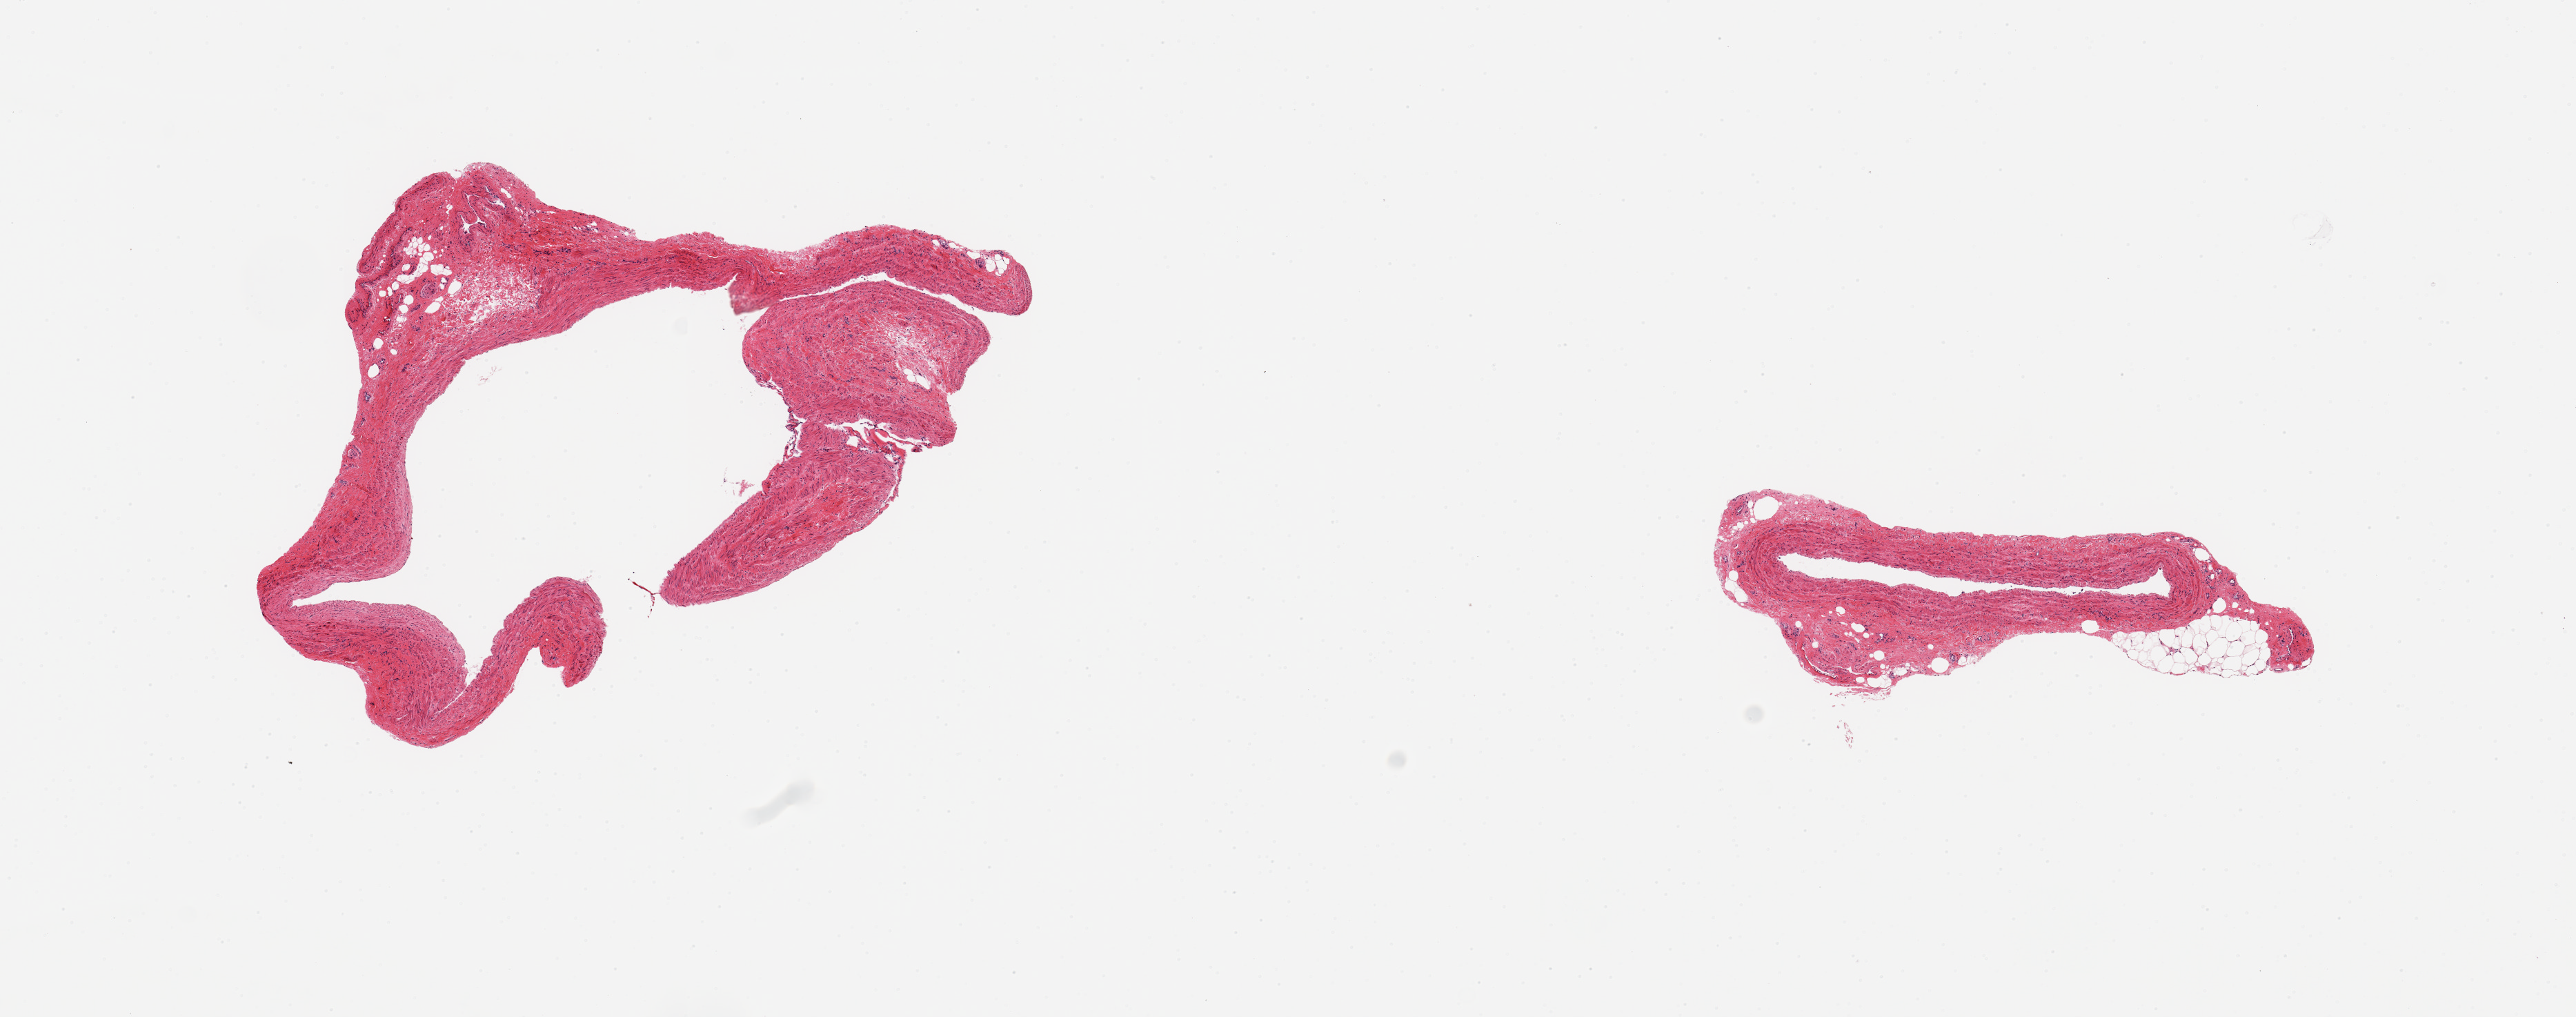
Haematoxylin and eosin whole-slide image — a low-resolution overview of the entire scanned area, about 14.8 x 5.8 mm. PAXgene-fixed, paraffin-embedded tissue. Section of tibial artery (target tissue). Donor tissue sample. Donor: female.
Review note (as recorded): 2 pieces.